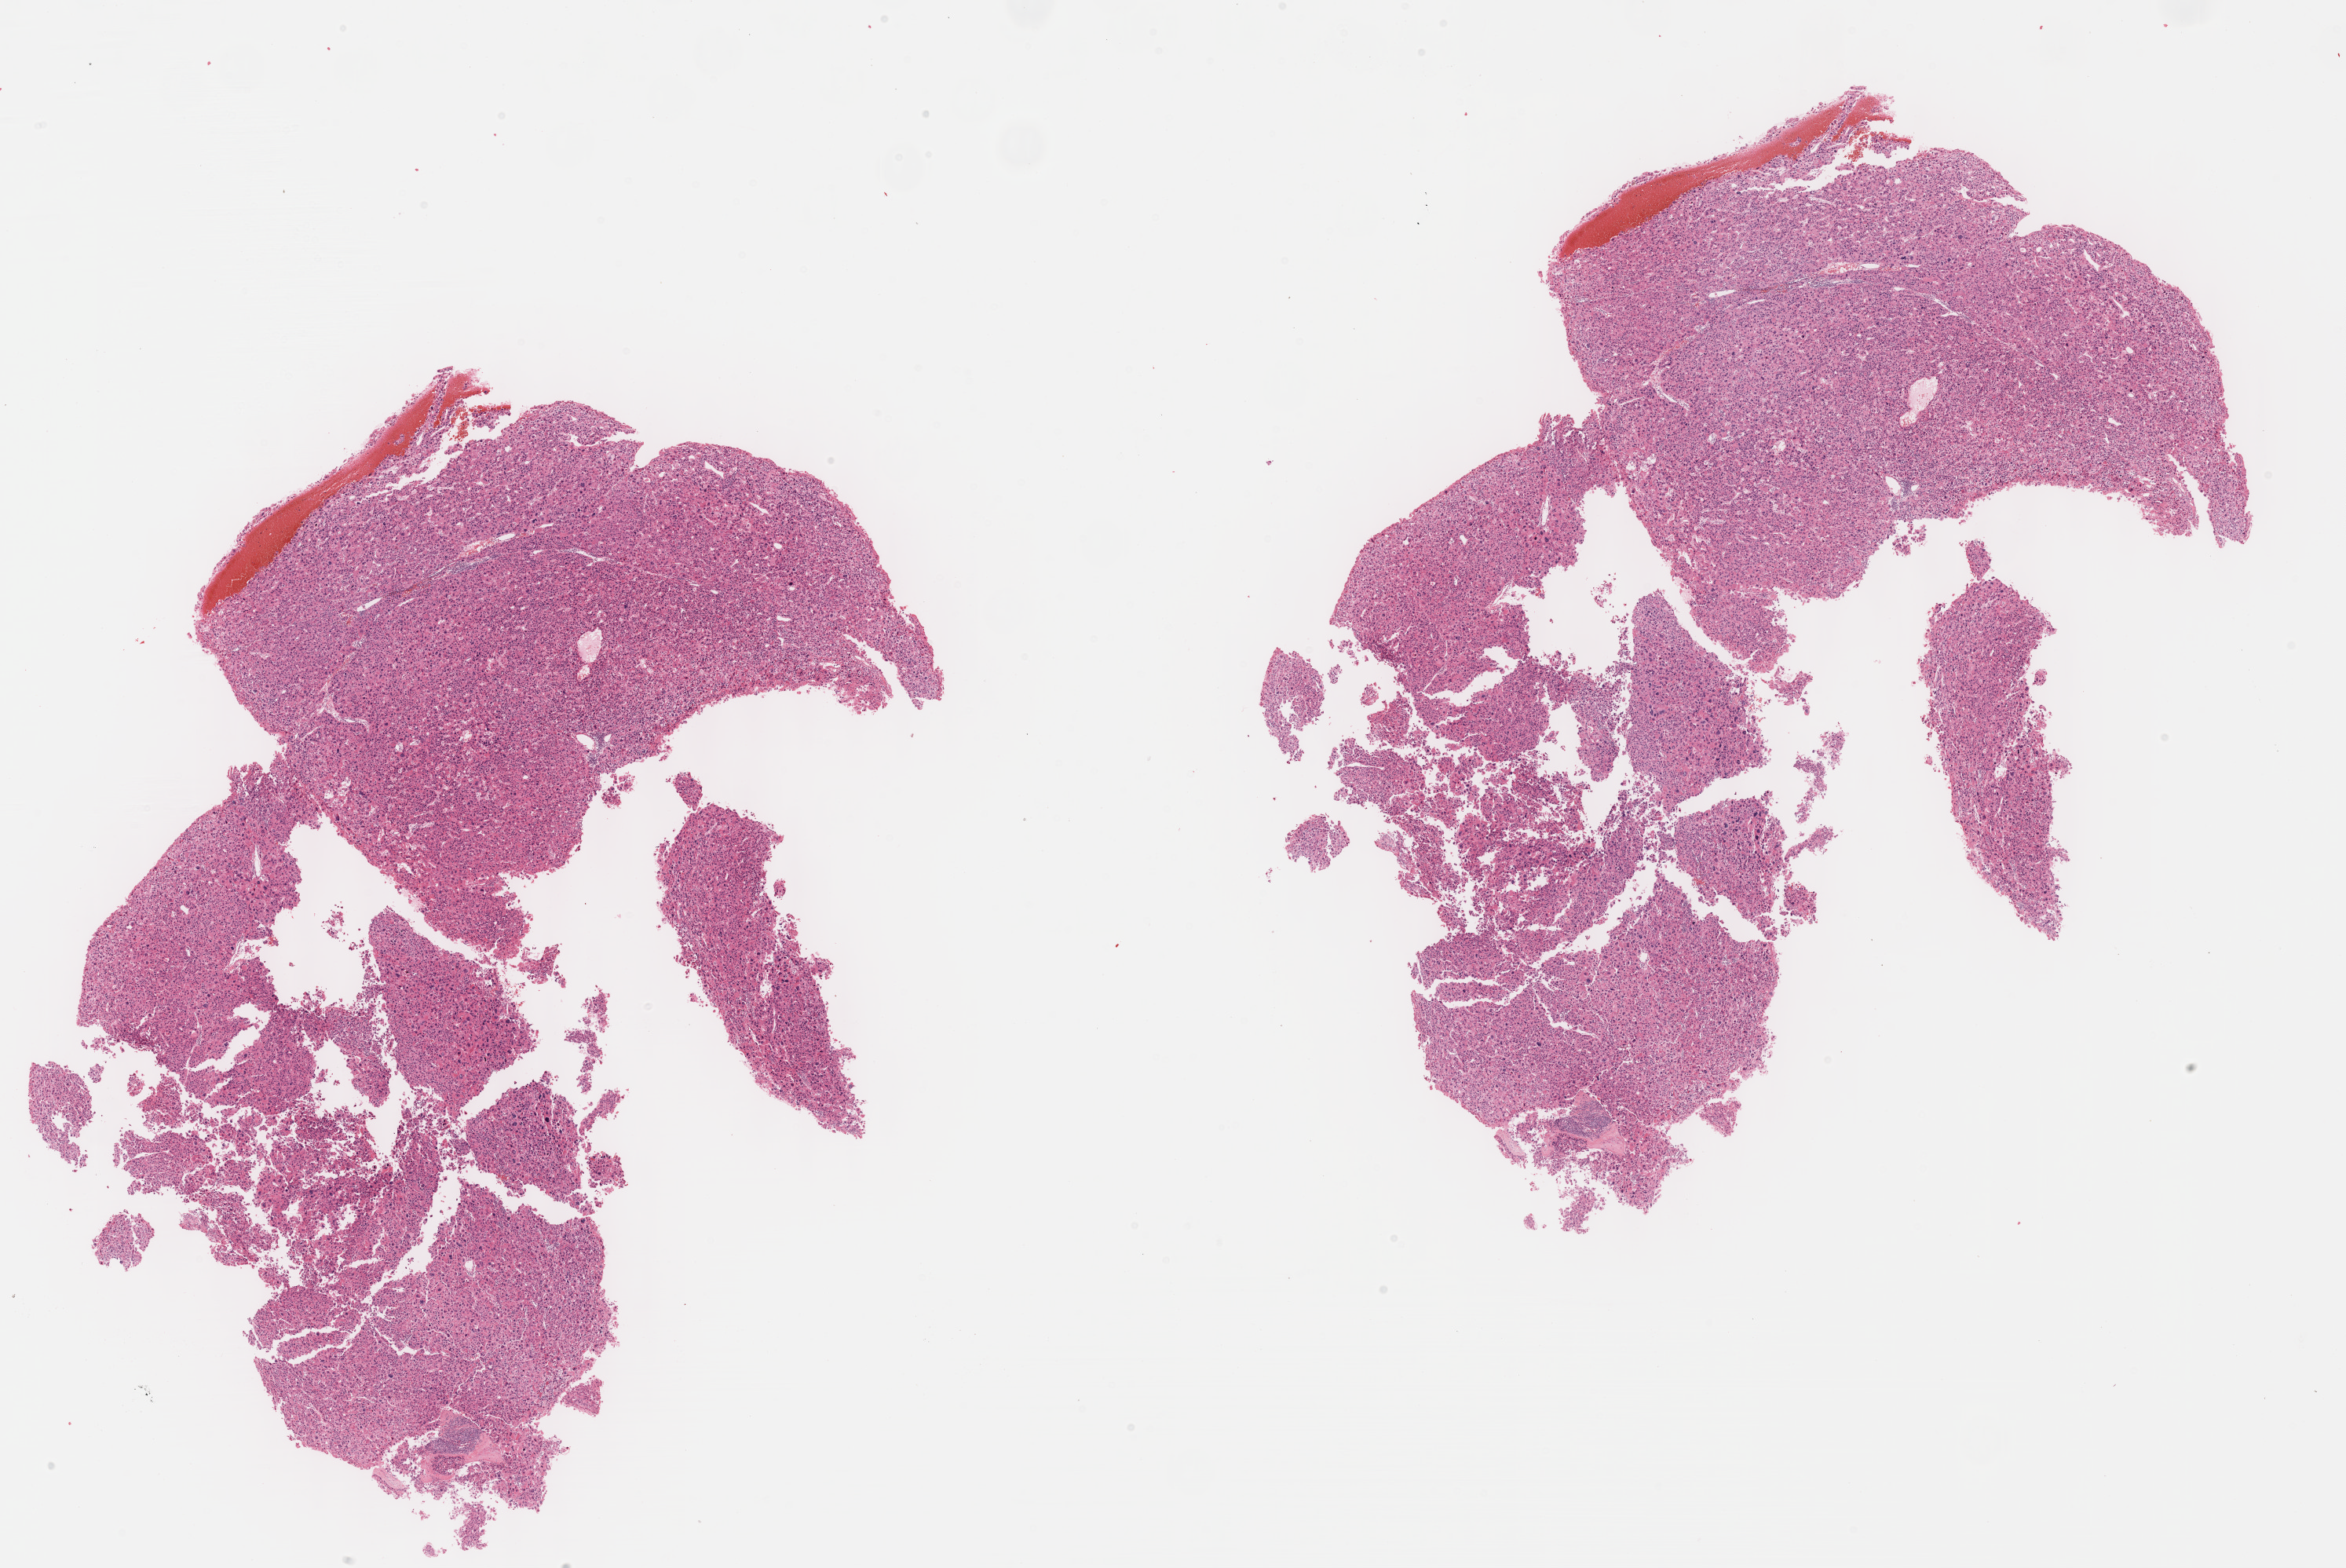
Digitized H&E-stained tissue section (whole slide) — a low-resolution overview of the entire scanned area, about 24.1 x 16.1 mm (from a 40x scan); formalin-fixed paraffin-embedded (FFPE) diagnostic section; liver, primary tumour sample. Female patient; age at initial diagnosis 64 years. Histologic grade: G4 (undifferentiated).
- AJCC pathologic stage: I (7th edition)
- histologic diagnosis: Hepatocellular carcinoma, NOS